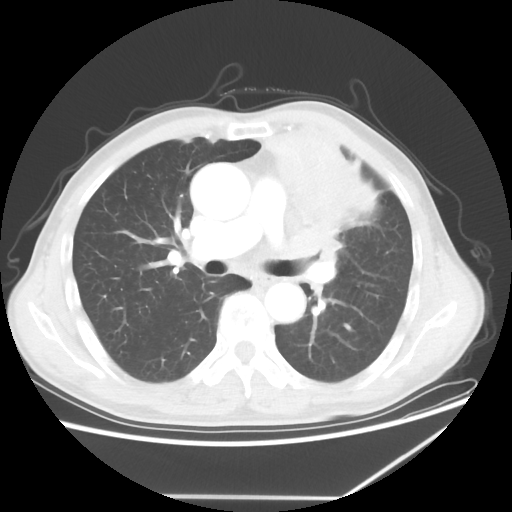
Chest CT, one axial slice. Slice 37 of 64 in the series (ordered by position). Reconstruction kernel STANDARD. 100 kVp. Lung window (W 1500 / L -600 HU). 512 × 512 image matrix, field of view 383 × 383 mm. Male patient, age 64 years. From the clinical record (not read from this slice): clinical TNM (as recorded): T1c N1 M1; histopathological grade: G2.
Structures marked on this image (bounding box drawn by a radiologist):
- lung tumour (recorded histology: squamous cell carcinoma): box from (x=254, y=112) to (x=413, y=289) px